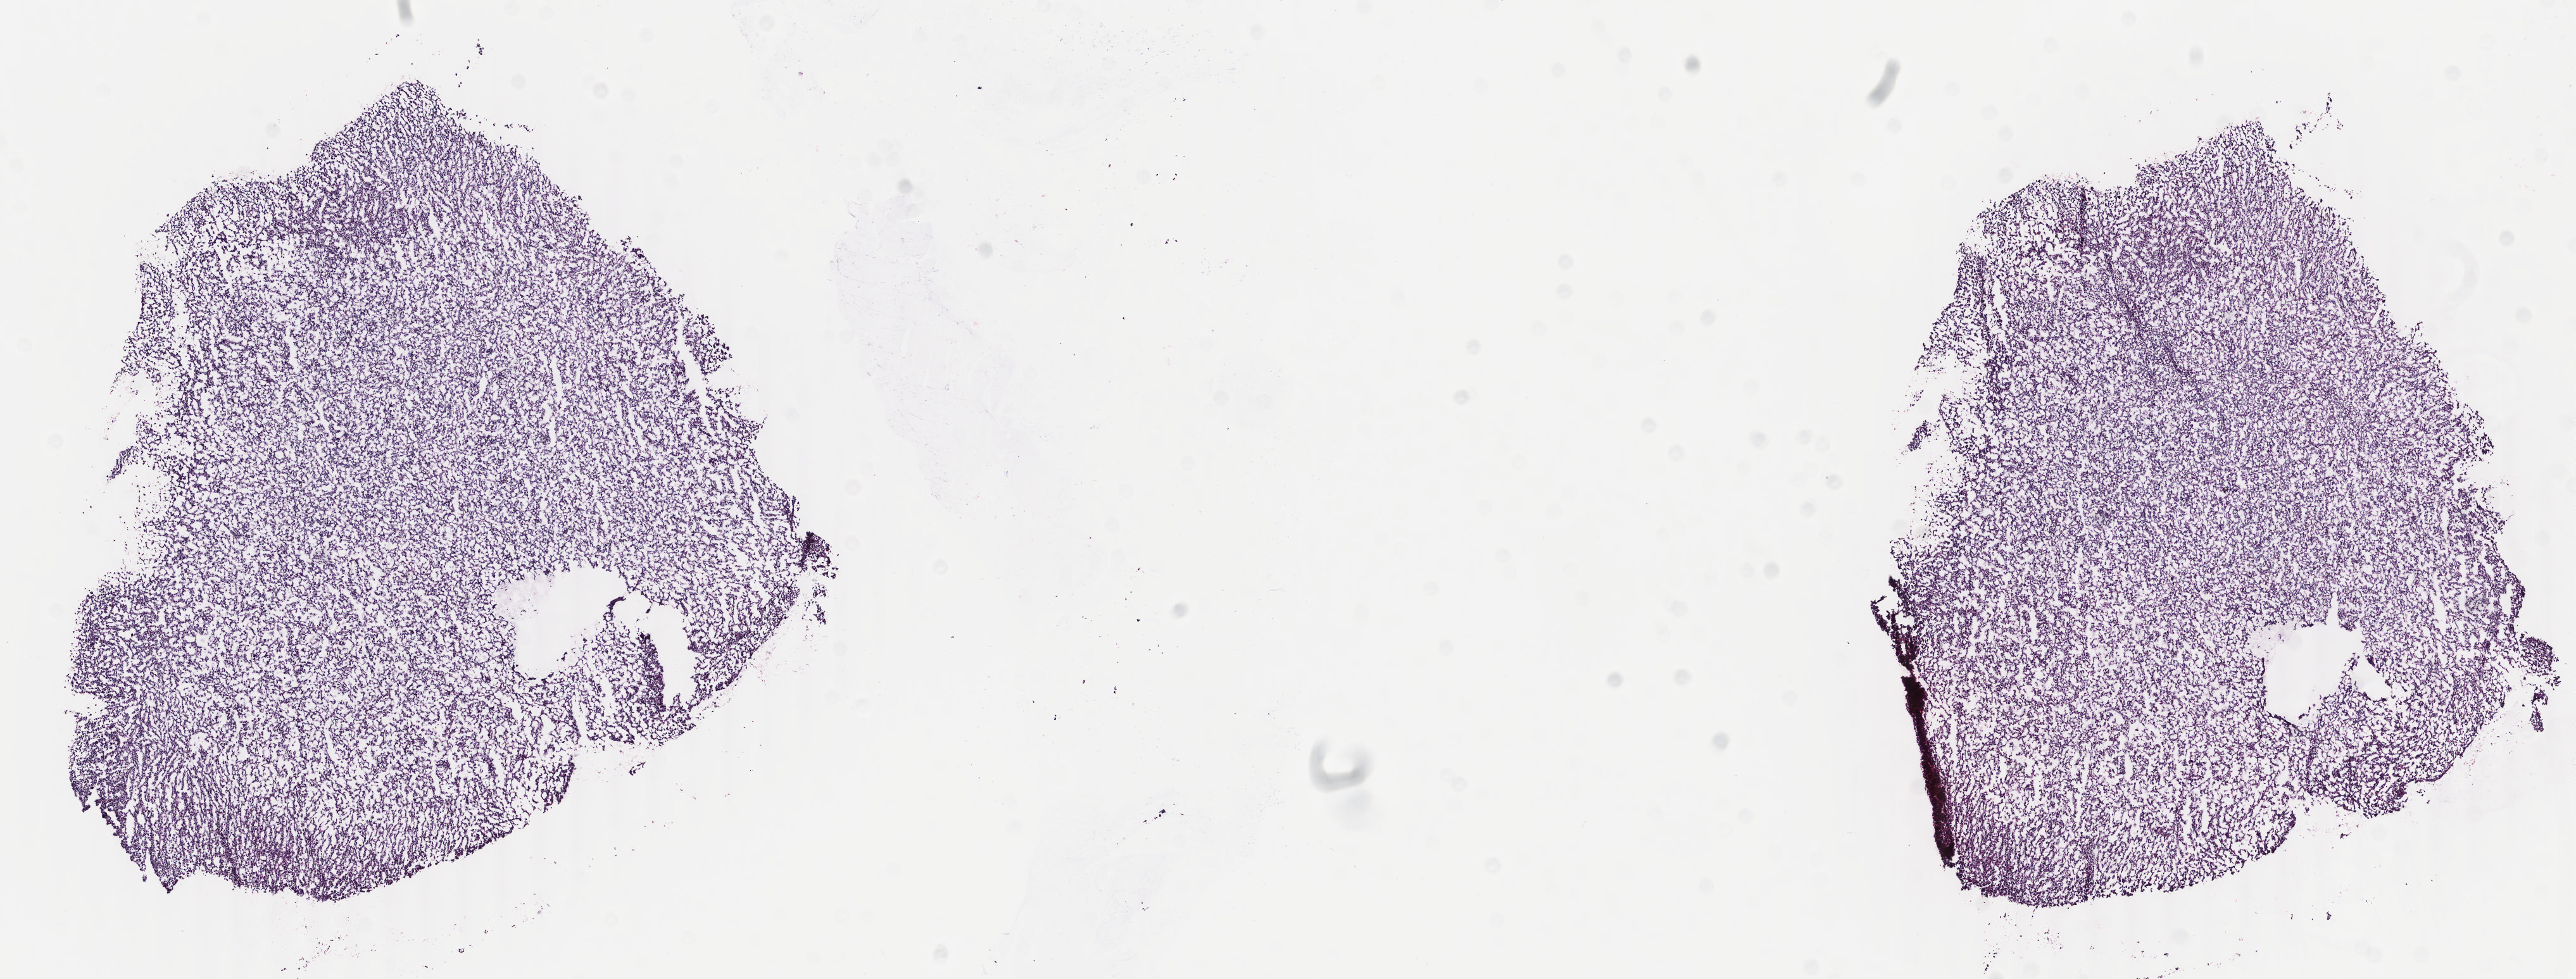
Digitized H&E tissue section (whole slide), a low-resolution overview of the entire scanned area, about 16.2 x 6.2 mm (acquisition: 40x scan). Frozen section. Metastatic tumour sample. Female, age 43 years at initial diagnosis. Composition of this section per pathologist review: tumour cells 90%, tumour nuclei 90%, normal cells 0%, stromal cells 10%, necrosis 0%. Infiltration values recorded for this section: lymphocyte infiltration 2%, monocyte infiltration 1%, neutrophil infiltration 1%.
This section: metastatic tumour tissue. Patient diagnosis: Malignant melanoma, NOS.